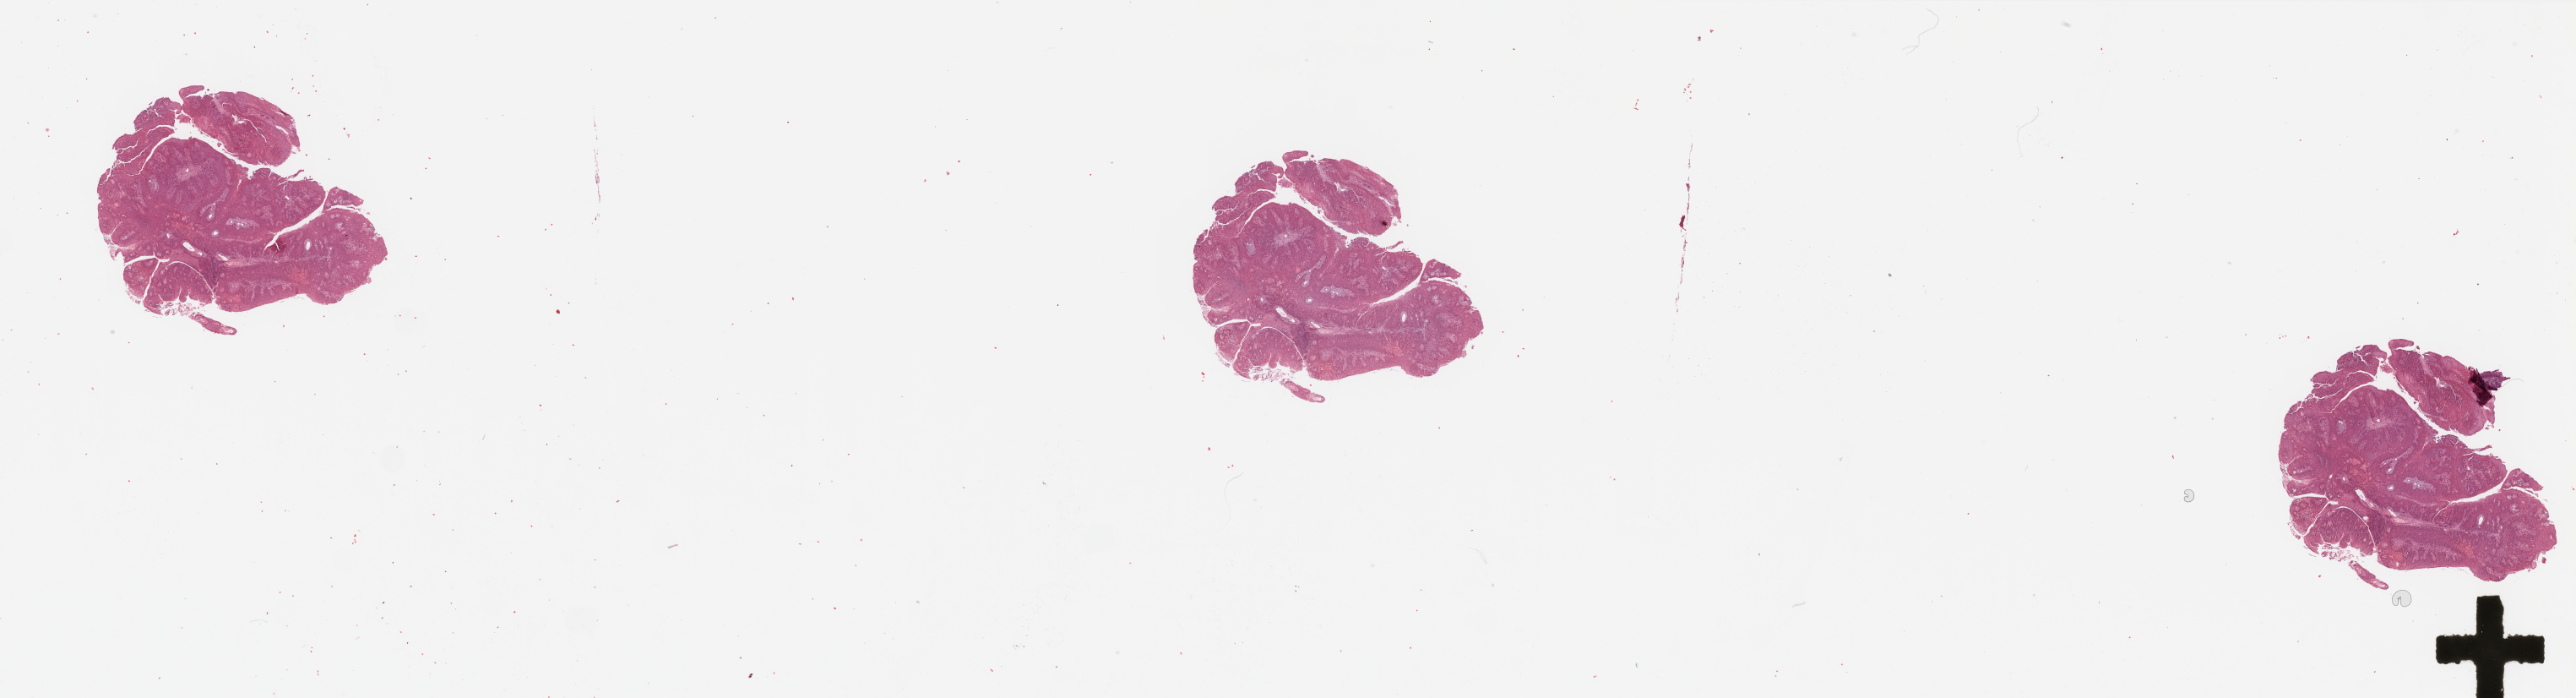
Digitized H&E-stained tissue section (whole slide), whole scanned area (about 48.2 x 13.1 mm, slide scanned at 20x) shown as a low-resolution overview. Tumour tissue sample, sampled site: larynx. Male, 42 y/o. Histologic grade: G2 (moderately differentiated). Pathologist review of this section (percent, as recorded): tumour nuclei 85%, necrosis 5%.
Primary tumour site (as recorded): larynx. Histologic diagnosis: Squamous cell carcinoma, NOS (larynx, NOS). AJCC pathologic stage: III.